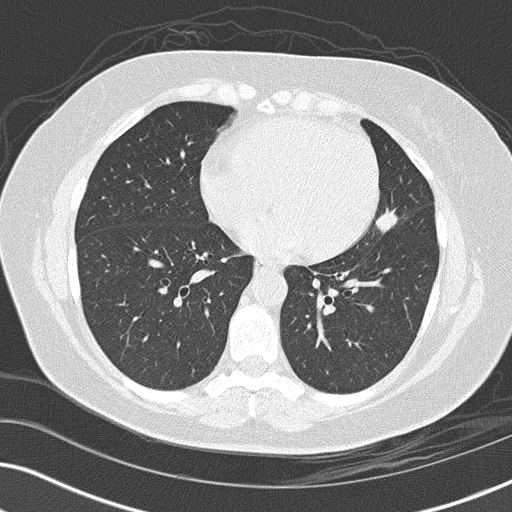
Axial slice from a low-dose chest CT screening exam. Third screening round (two years after baseline). Lung window (W 1500 / L -600 HU). 2 mm slice thickness. Lung (sharp) reconstruction kernel (B50f). 120 kVp. 512 × 512 image matrix, field of view 330 × 330 mm. Female participant, aged 56 years at enrolment. Former smoker at enrolment.
• Expert reader's lesion annotation, box from (x=357, y=199) to (x=411, y=247) px.
• Reader record for this screening exam (exam-level; its link to the box is not recorded): non-calcified nodule or mass ≥4 mm, lingula, 14 × 14 mm, spiculated (stellate) margins, soft tissue attenuation, pre-existing on the prior screen: yes; interval growth: yes.
• Lung cancer was diagnosed 86 days after this screen: adenocarcinoma, NOS, left upper lobe, poorly differentiated (G3), stage IIIA (AJCC 6th edition), 15 mm at pathology.